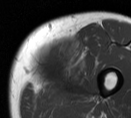
MRI of an extremity soft-tissue mass, one axial slice. Slice 17 of 55 in the series (ordered by position). MR volume resampled by the dataset authors to the PET/CT grid (not the native acquisition matrix). 3.27 mm slice thickness. 131 × 118 image matrix, field of view 128 × 115 mm. Male patient. From the clinical record (not read from this slice): histological type: pleiomorphic liposarcoma; grade: high; site of the primary tumour: left thigh.
Annotated regions visible in this slice (expert contour drawn on MRI and transferred to this co-registered scan by the dataset authors):
- gross tumour volume including surrounding oedema: bounding box <27,41,94,101> (left, top, right, bottom; pixels)
- gross tumour volume (mass): <27,40,71,90>